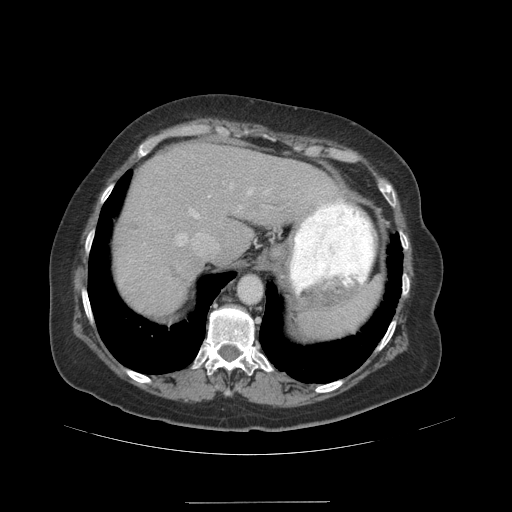
Contrast-enhanced abdominal CT (liver protocol), one axial slice; reconstruction kernel STANDARD; 140 kVp; soft-tissue window (W 400 / L 40 HU); 512 × 512 image matrix. From the clinical record (not read from this slice): diagnosis: hepatocellular carcinoma (patient treated with transarterial chemoembolisation; whether this scan precedes or follows treatment is not stated here); TNM stage (as recorded): Stage-IVA; Child-Pugh class: A.
Annotated regions visible in this slice (semi-automatically segmented with operator editing):
- abdominal aorta: bounding box [x1, y1, x2, y2] px = [238, 275, 261, 304]
- liver parenchyma outside the tumour (the mass and vessels are separate outlines, so this box may not span the whole liver): [114, 142, 336, 316]
- liver vessels: [178, 186, 324, 246]